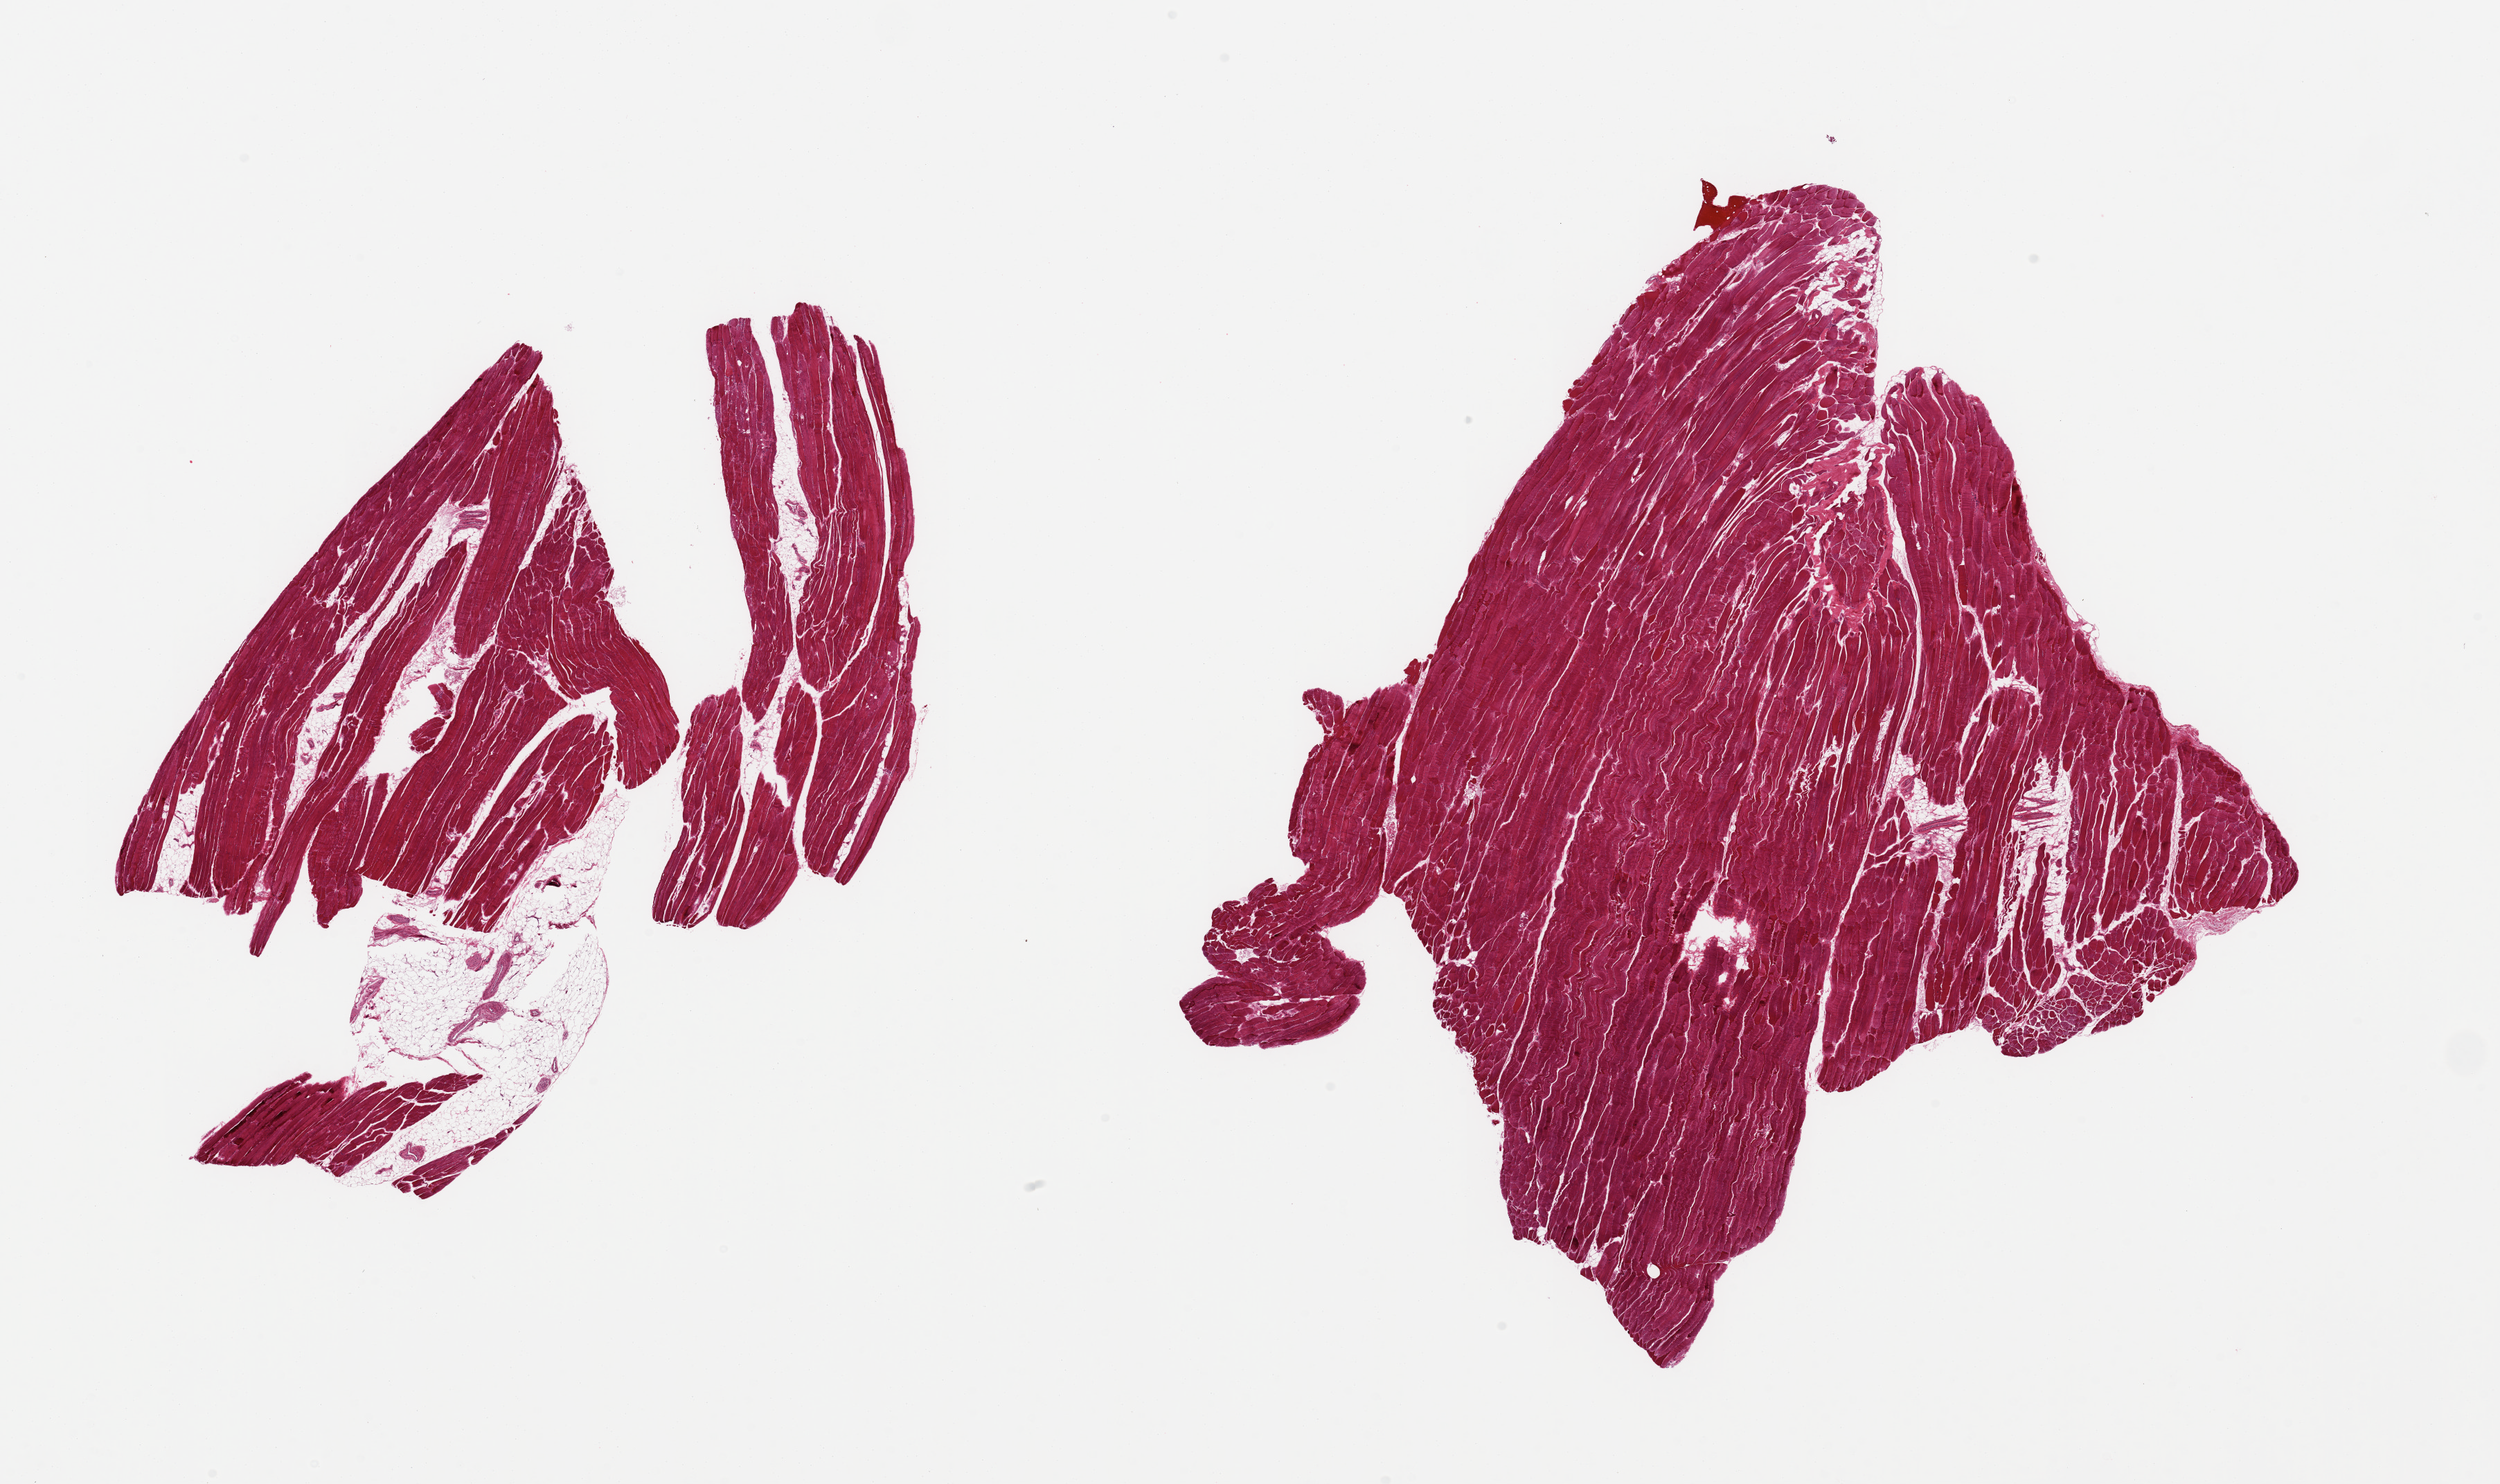
Digitized haematoxylin and eosin-stained section, a low-resolution overview of the entire scanned area, about 28.5 x 16.9 mm (acquisition: 20x scan); PAXgene-fixed, paraffin-embedded tissue; section of skeletal muscle (target tissue); donor tissue sample.
- review note (as recorded): 2 pieces; 1 piece has 30% internal fat content